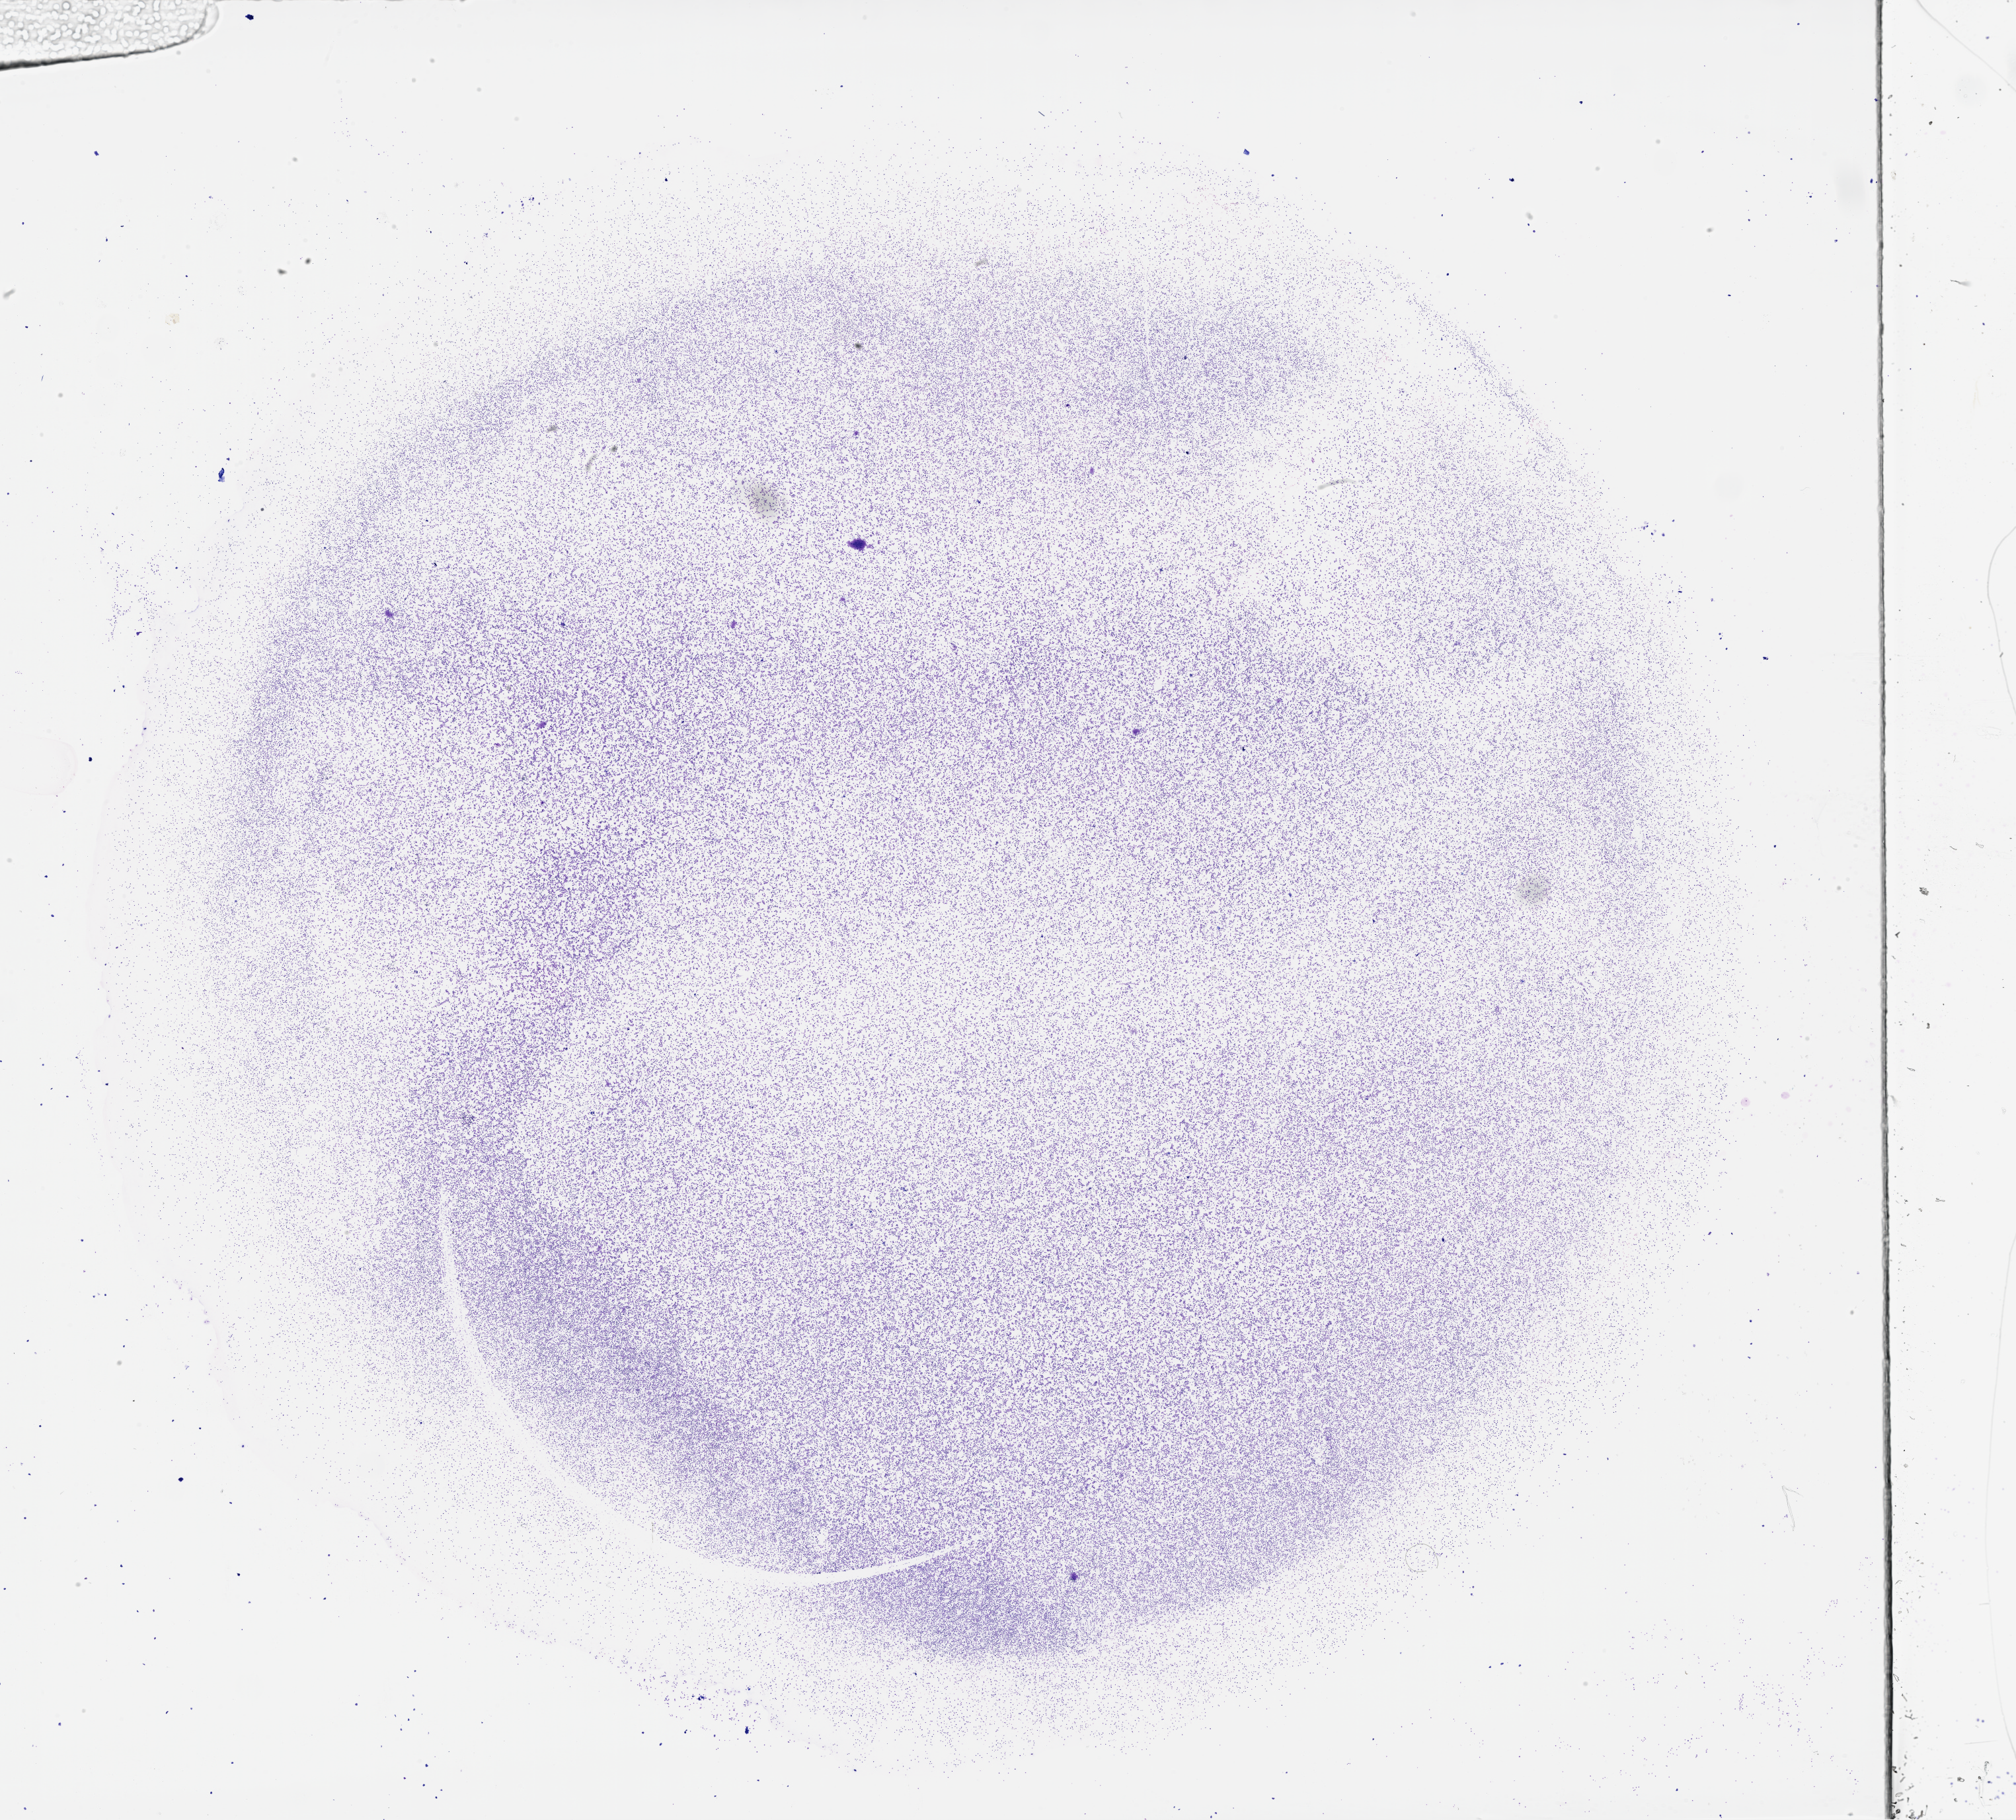
H&E whole-slide image, a low-resolution overview of the entire scanned area, about 24.6 x 22.2 mm (slide scanned at 40x). Bone marrow (leukaemic) sample. Female, 77 y/o. Blasts: 40%.
WHO classification: AML without maturation. Diagnosis: Acute Myeloid Leukemia. FAB classification: M2.